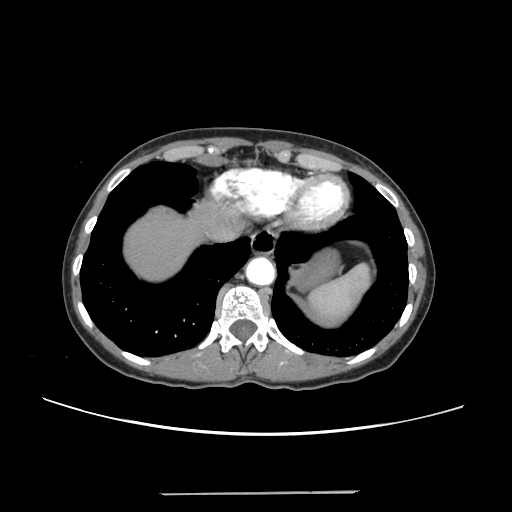
Contrast-enhanced abdominal CT, one axial slice; intravenous contrast given; soft-tissue window (W 400 / L 40 HU); 512 × 512 image matrix, field of view 371 × 371 mm. Female patient, age 60 years. Case-level facts recorded for this patient, not image findings: diagnosis: colorectal cancer liver metastases, imaged before liver resection; multiple liver metastases: no; largest metastasis: 1.5 cm; disease in both lobes: no.
Annotated regions visible in this slice (manually delineated by an expert):
- liver: bounding box <125,205,227,281> (left, top, right, bottom; pixels)
- planned liver remnant (the part of the liver to remain after resection): <125,205,226,281>